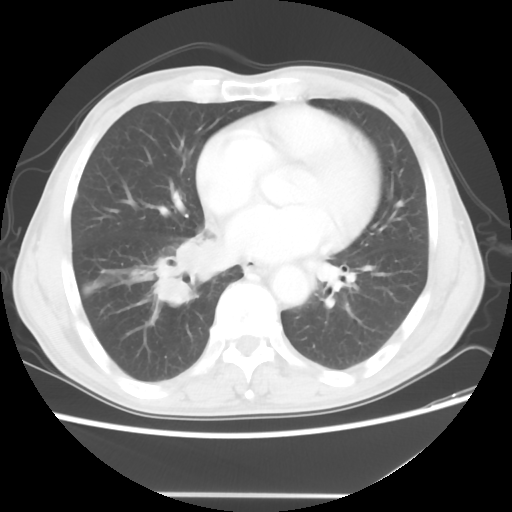
Chest CT, one axial slice; position 23 of 56 along the scan axis; reconstruction kernel STANDARD; 120 kVp; lung window (W 1500 / L -600 HU); 512 × 512 image matrix, field of view 344 × 344 mm. Male patient, age 65 years. From the clinical record (not read from this slice): clinical TNM (as recorded): T1c N3 M0.
Structures marked on this image (rectangle marked by the reading radiologist):
- lung tumour (recorded histology: small cell carcinoma): box from (x=148, y=231) to (x=228, y=306) px